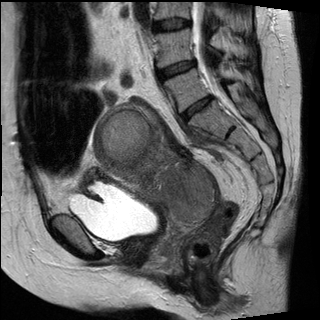
Pelvic MRI for cervical cancer, one sagittal slice. Position 14 of 30 along the scan axis. T2-weighted. 1.5 T. TE 89 ms, TR 2930 ms. 4 mm slice thickness. 320 × 320 image matrix. Patient: female, 62 years.
Outlined on this slice (manually delineated by an expert):
- uterus and cervix: bounding box <91,102,214,226> (left, top, right, bottom; pixels)